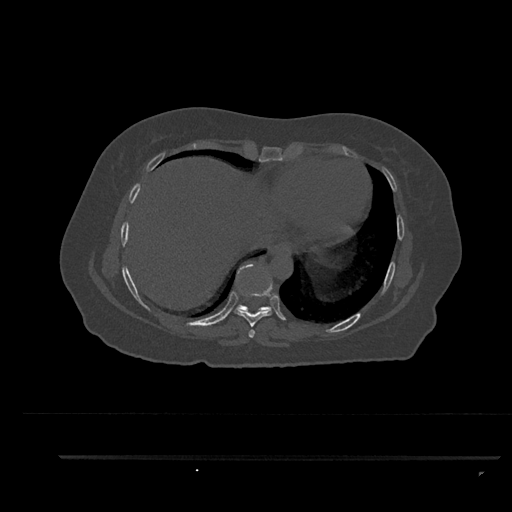
CT including the spine, one axial slice; reconstruction kernel Br40s/3; bone window (W 1800 / L 400 HU); 0.5 mm slice thickness; 512 × 512 image matrix, field of view 408 × 408 mm. Female patient, age 44 years. Case-level facts recorded for this patient, not image findings: primary cancer: renal.
Outlined on this slice (semi-automatically segmented with operator editing):
- T7 vertebra: box from (x=248, y=329) to (x=255, y=338) px
- T8 vertebra: (x=234, y=268)–(x=273, y=328)
- T9 vertebra: (x=235, y=304)–(x=272, y=313)